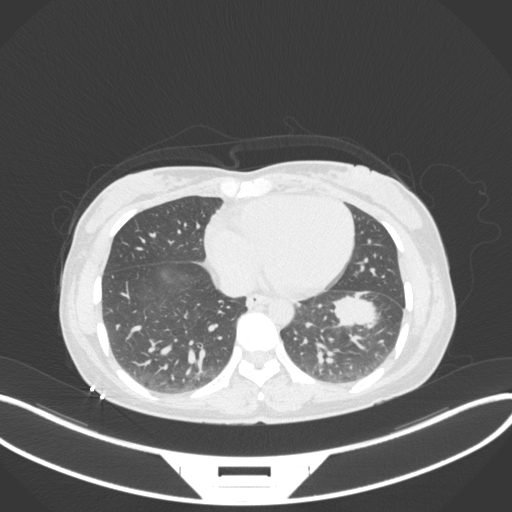
Chest CT, one axial slice; position 125 of 361 along the scan axis; reconstruction kernel B31f; lung window (W 1500 / L -600 HU); 1 mm slice thickness; 512 × 512 image matrix, field of view 400 × 400 mm. Female patient, age 41 years. Case-level facts recorded for this patient, not image findings: clinical TNM (as recorded): T2a N3 M1b.
Annotated regions visible in this slice (rectangle marked by the reading radiologist):
- lung tumour (recorded histology: adenocarcinoma): bounding box <330,290,380,330> (left, top, right, bottom; pixels)